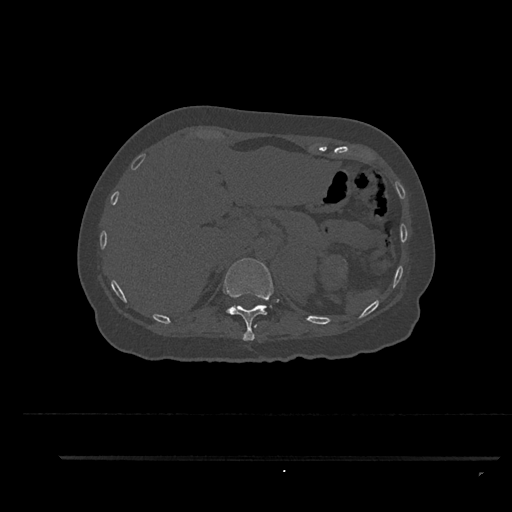
CT including the spine, one axial slice; slice 308 of 797 in the series (ordered by position); reconstruction kernel Br40s/3; 120 kVp; bone window (W 1800 / L 400 HU); 0.5 mm slice thickness; 512 × 512 image matrix. Patient: female, 44 years. From the clinical record (not read from this slice): primary cancer: renal; vertebrae with lytic lesions (as recorded): L1.
Structures marked on this image (semi-automatic segmentation, software-assisted and operator-edited):
- T11 vertebra: bounding box (x1, y1, x2, y2) in pixels: (223, 258, 274, 341)
- T12 vertebra: (225, 307, 231, 320)